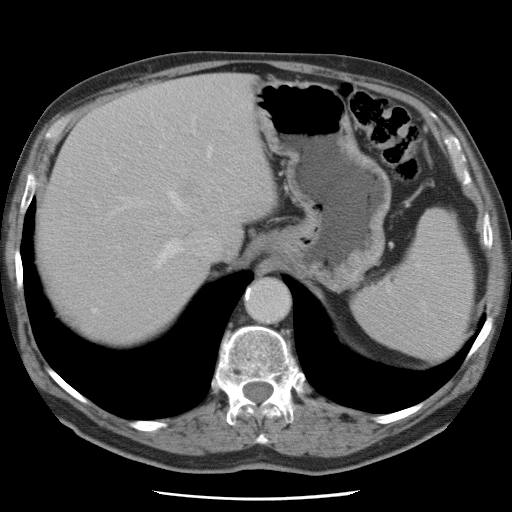
Contrast-enhanced abdominal CT, one axial slice. Slice 59 of 78 in the series (ordered by position). Intravenous contrast given. Soft-tissue window (W 400 / L 40 HU). 5 mm slice thickness. 512 × 512 image matrix, field of view 337 × 337 mm. Male patient, age 75 years. Case-level facts recorded for this patient, not image findings: diagnosis: colorectal cancer liver metastases, imaged before liver resection; multiple liver metastases: yes; largest metastasis: 2.4 cm; chemotherapy before resection: yes.
Annotated regions visible in this slice (expert manual segmentation):
- hepatic veins: bounding box (x1, y1, x2, y2) in pixels: (109, 146, 212, 269)
- liver: (39, 75, 273, 342)
- planned liver remnant (the part of the liver to remain after resection): (40, 133, 206, 341)
- portal vein (with intrahepatic branches): (112, 169, 115, 172)
- liver metastasis: (90, 307, 100, 314)
- liver metastasis: (183, 181, 197, 196)